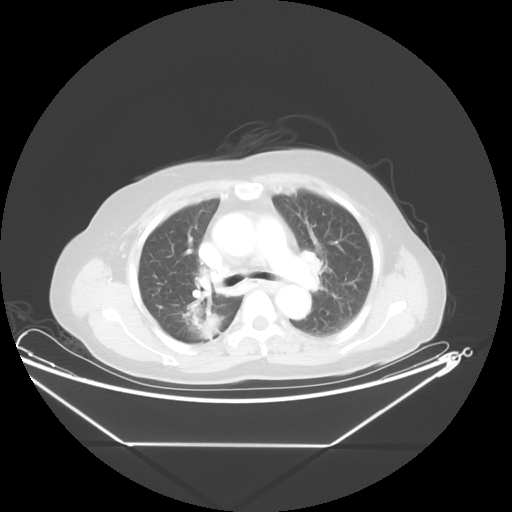
Chest CT, one axial slice; position 30 of 48 along the scan axis; reconstruction kernel STANDARD; 100 kVp; lung window (W 1500 / L -600 HU); 5 mm slice thickness; 512 × 512 image matrix, field of view 462 × 462 mm. Patient: female, 62 years. Case-level facts recorded for this patient, not image findings: clinical TNM (as recorded): T1c N0 M0; histopathological grade: G2-3.
Outlined on this slice (rectangle marked by the reading radiologist):
- lung tumour (recorded histology: adenocarcinoma): bounding box [x1, y1, x2, y2] px = [181, 305, 239, 351]